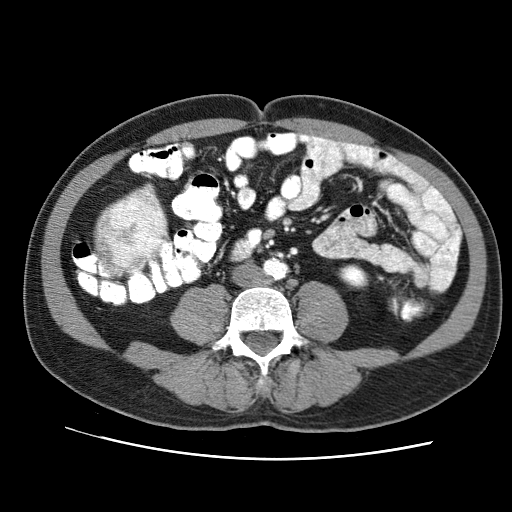
Contrast-enhanced abdominal CT (liver protocol), one axial slice; position 7 of 71 along the scan axis; reconstruction kernel STANDARD; 120 kVp; soft-tissue window (W 400 / L 40 HU); 512 × 512 image matrix, field of view 360 × 360 mm. From the clinical record (not read from this slice): diagnosis: hepatocellular carcinoma (patient treated with transarterial chemoembolisation; whether this scan precedes or follows treatment is not stated here); TNM stage (as recorded): Stage-II; Child-Pugh class: A; tumour nodularity: multinodular; tumour size: 4.6 cm.
Structures marked on this image (semi-automatic segmentation, software-assisted and operator-edited):
- mass: bounding box (x1, y1, x2, y2) in pixels: (94, 190, 165, 275)